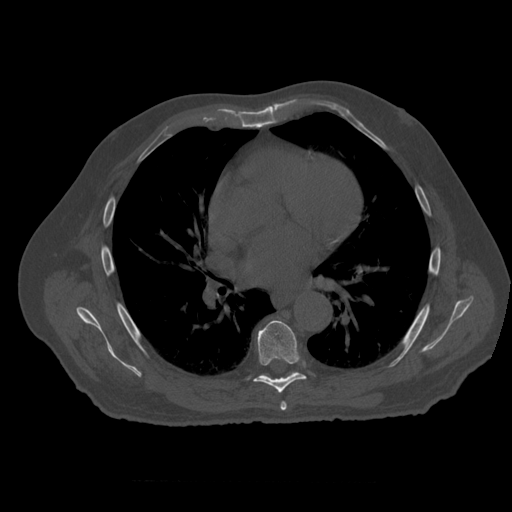
CT including the spine, one axial slice; slice 360 of 399 in the series (ordered by position); reconstruction kernel STANDARD; 120 kVp; bone window (W 1800 / L 400 HU); 1.25 mm slice thickness; 512 × 512 image matrix, field of view 407 × 407 mm. Patient age 73 years. Case-level facts recorded for this patient, not image findings: primary cancer: prostate; vertebrae with lytic lesions (as recorded): L2.
Annotated regions visible in this slice (semi-automatic segmentation, software-assisted and operator-edited):
- T6 vertebra: bounding box (x1, y1, x2, y2) in pixels: (281, 402, 287, 413)
- T7 vertebra: (254, 321, 307, 393)